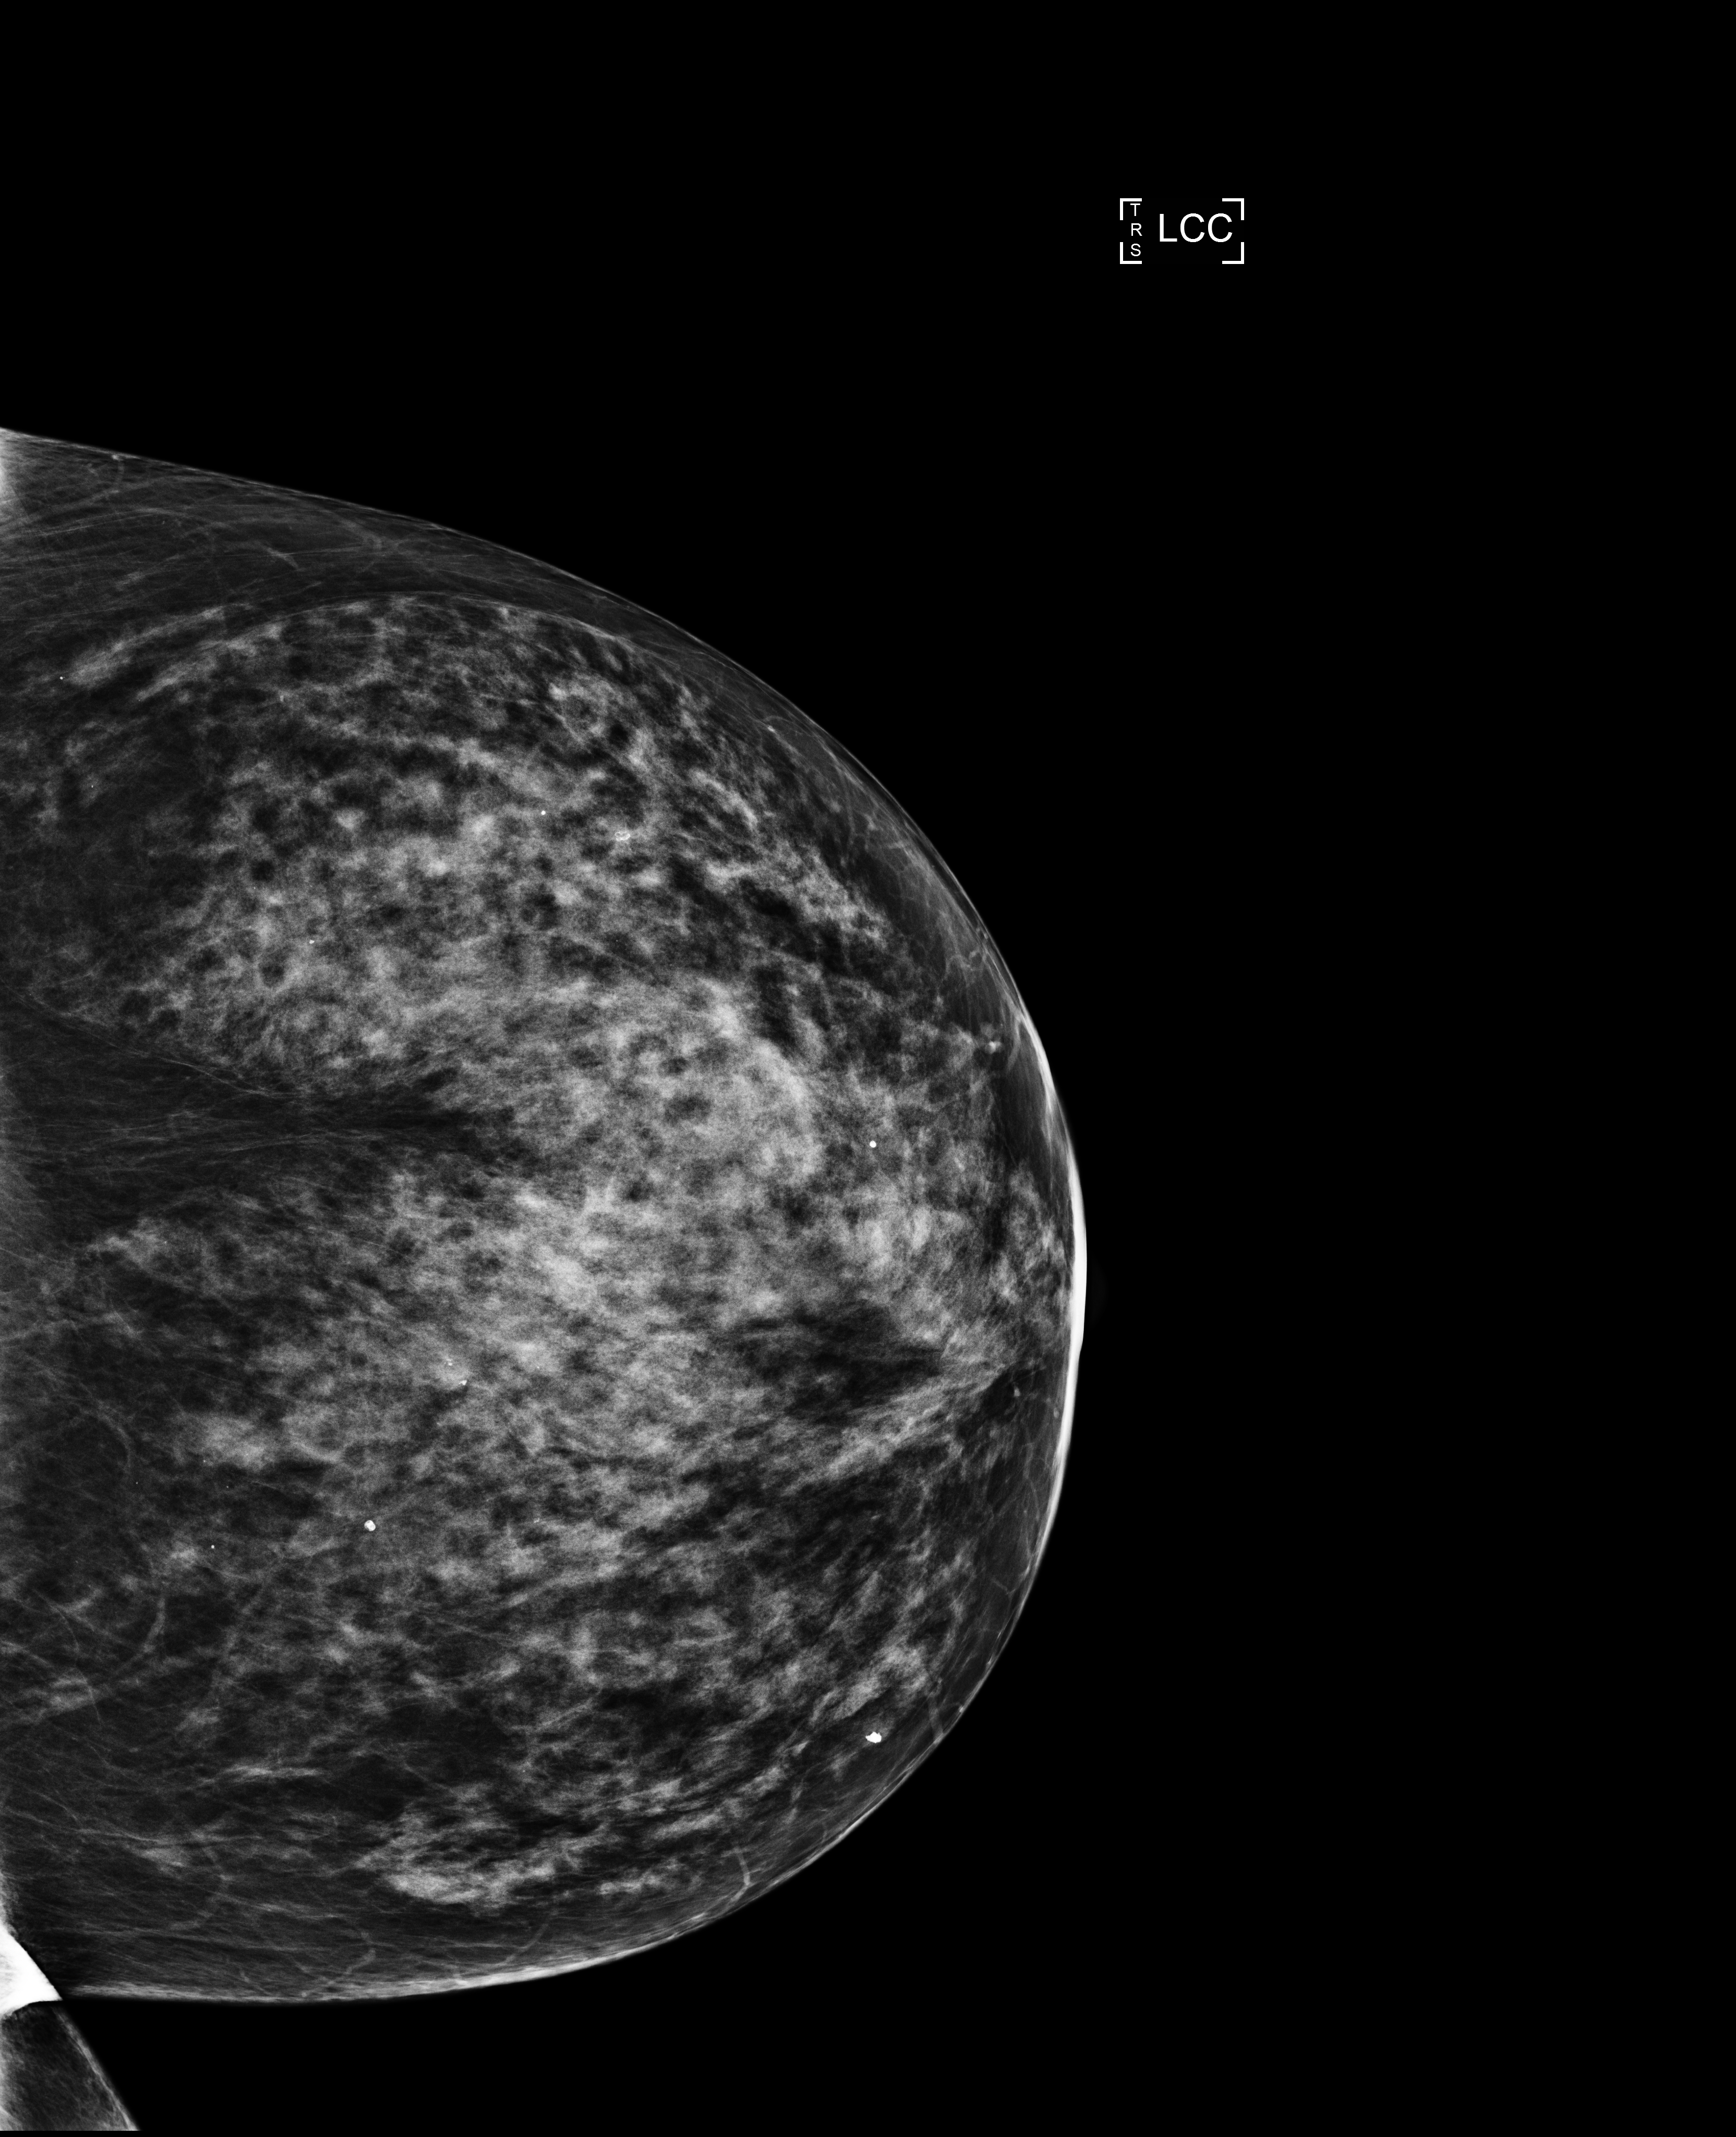
Screening examination; system: Selenia Dimensions. Patient aged 63 years (female).
Image type: full-field digital mammogram. Breast: left. Projection: cranio-caudal projection.